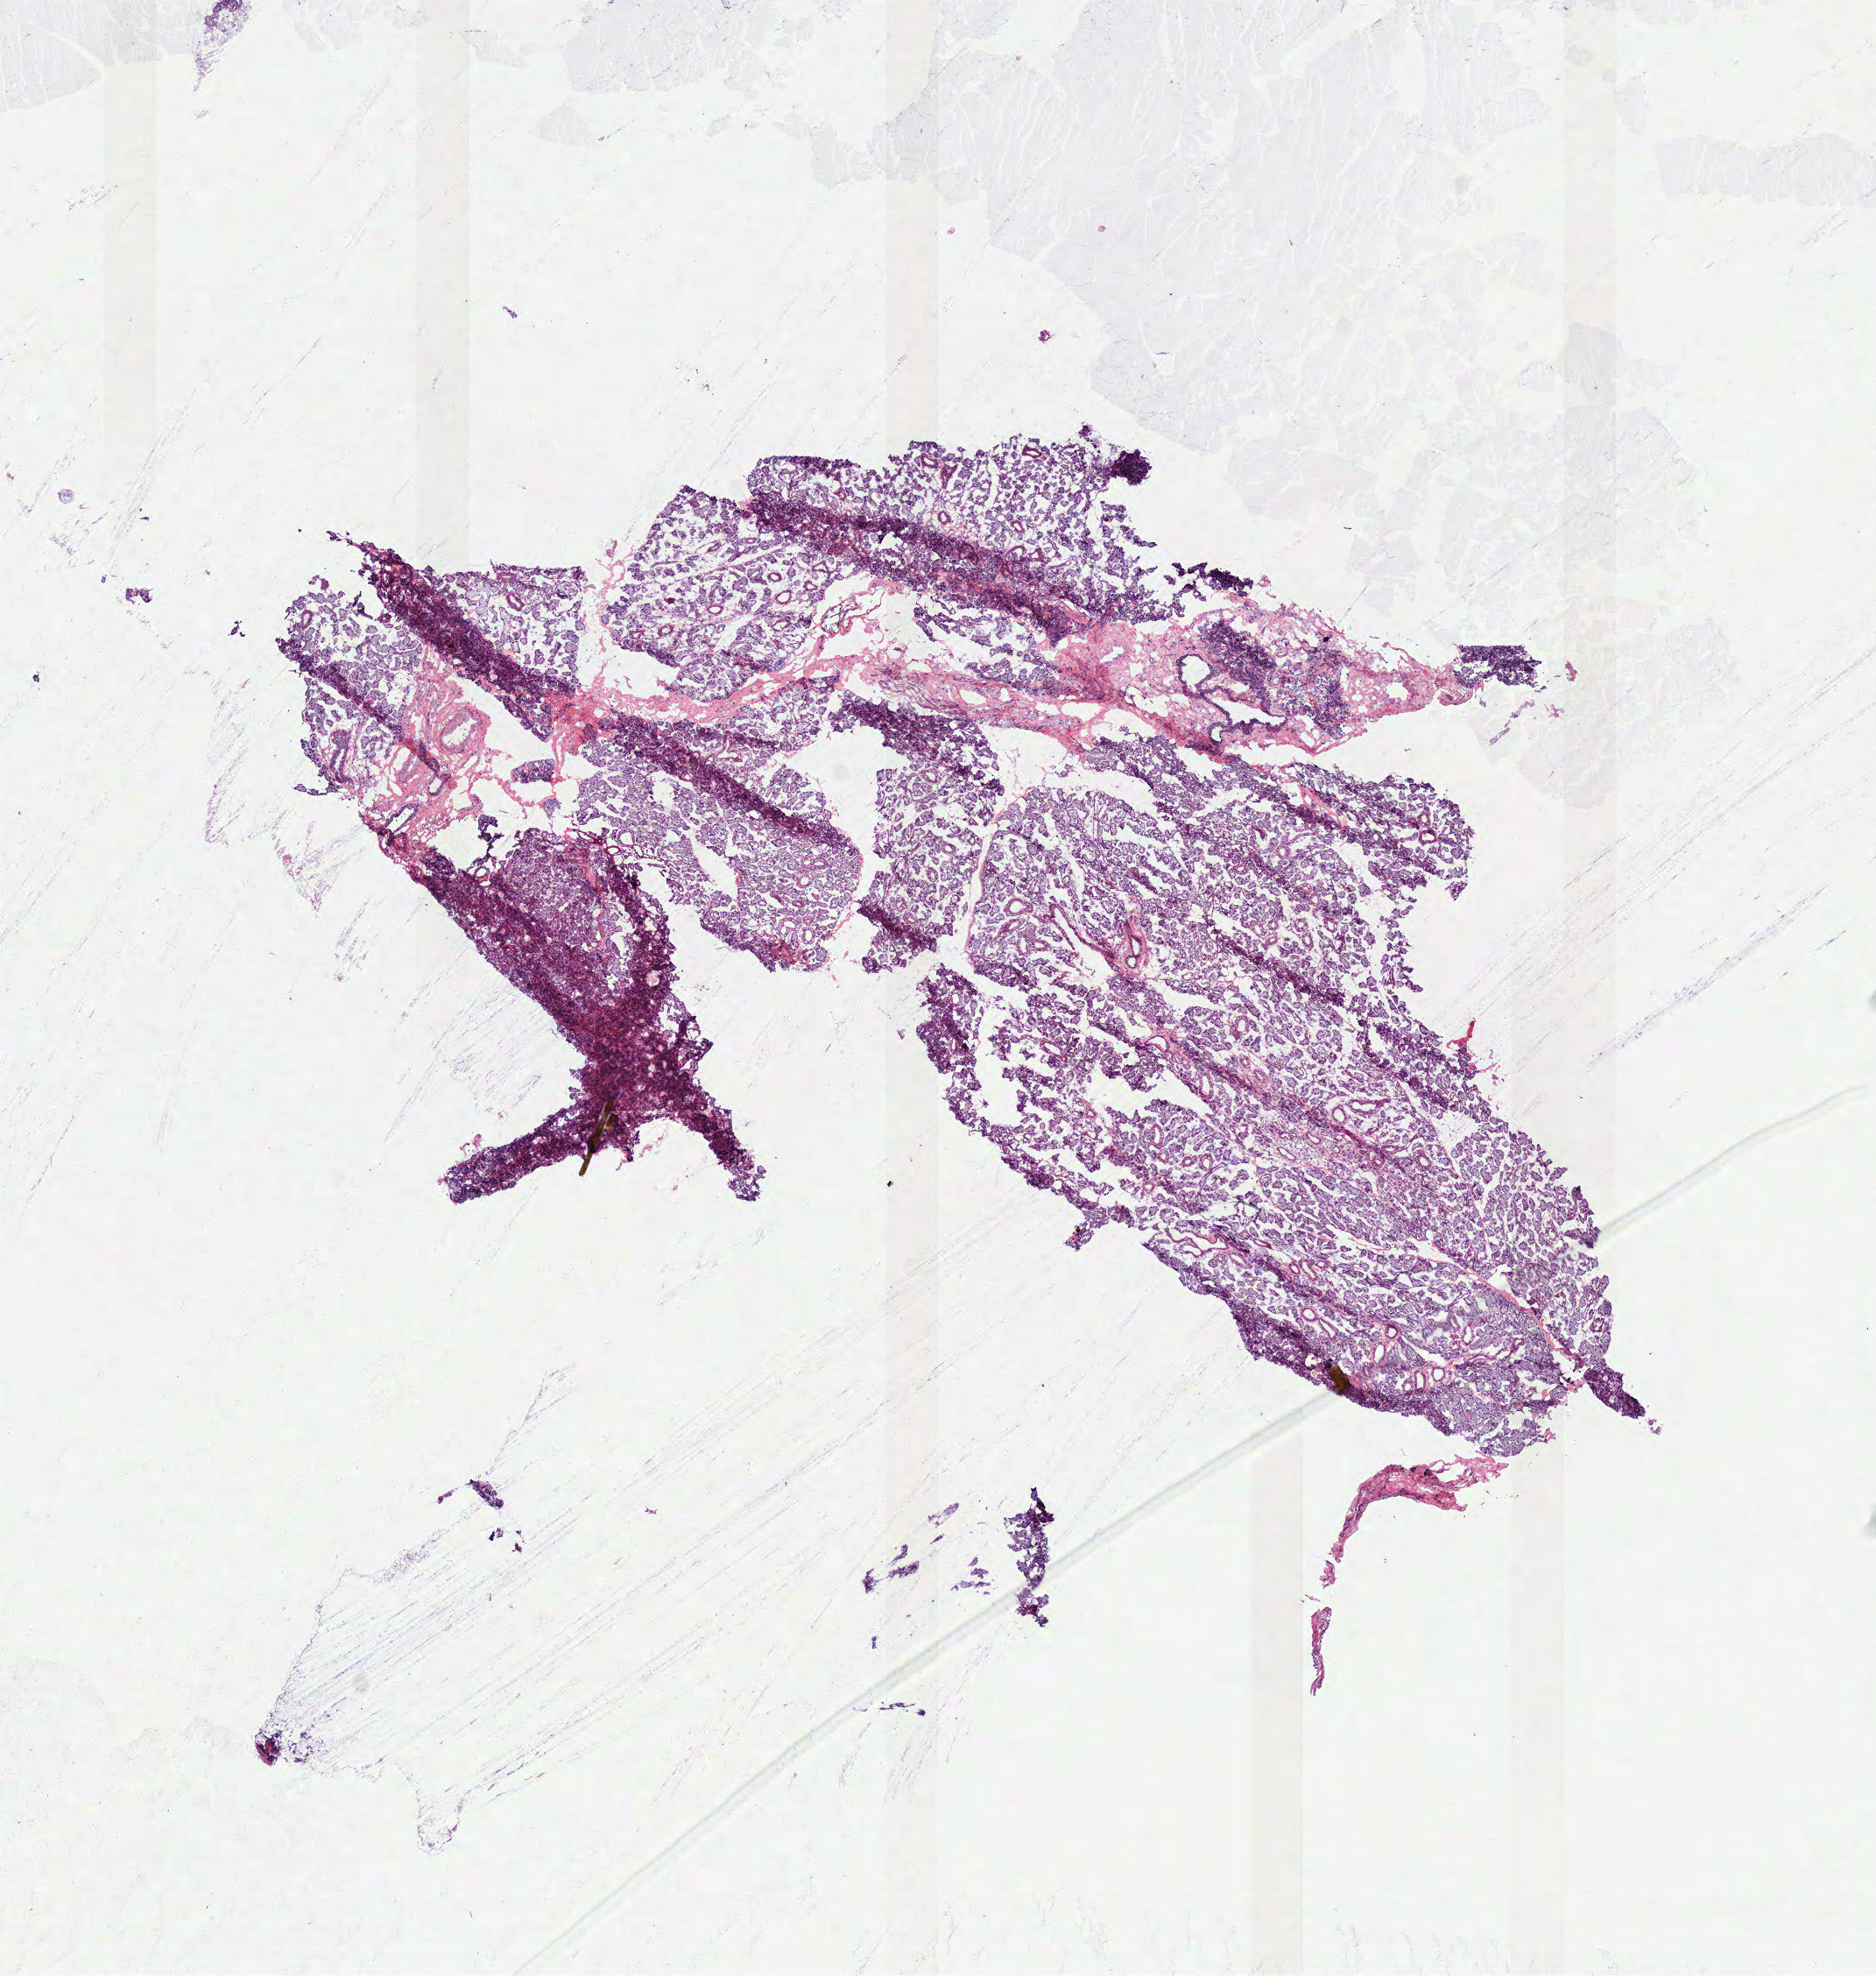
Digitized H&E tissue section (whole slide) — low-resolution overview of the scanned area, about 8.4 x 8.9 mm (acquisition: 40x scan), frozen section from the top of the tissue portion, sample: solid tissue normal (non-tumour tissue), head and neck. Male, age 53 years at initial diagnosis.
- this section: solid tissue normal sample (biorepository sample class)
- patient diagnosis: Squamous cell carcinoma, NOS